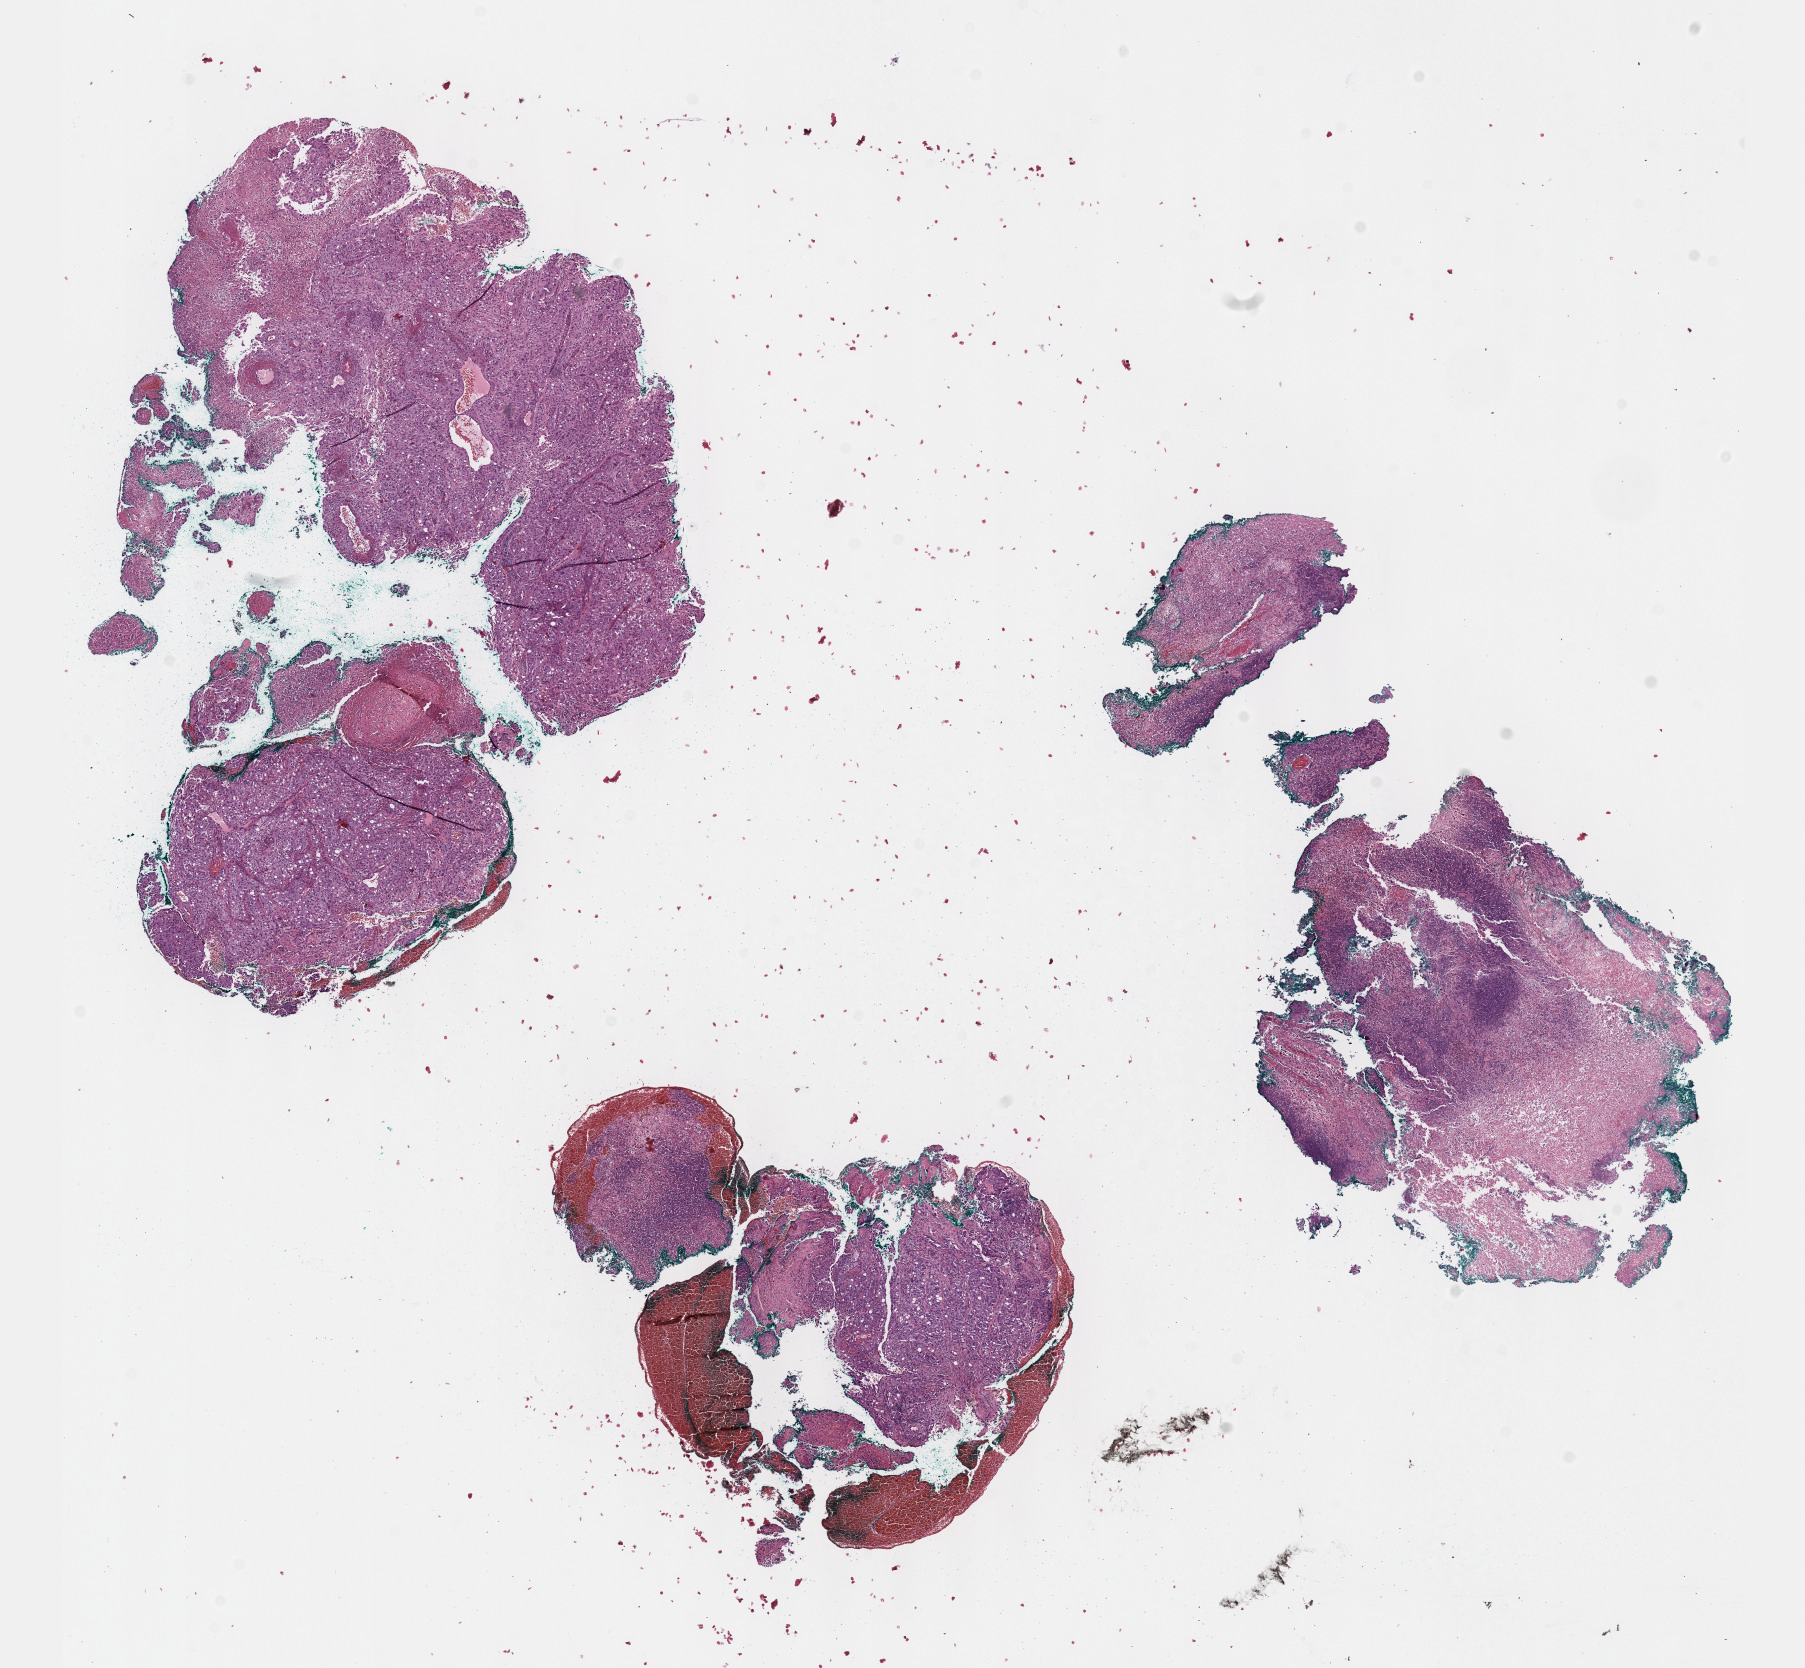
H&E whole-slide image — low-resolution overview of the scanned area, about 14.6 x 13.5 mm, formalin-fixed paraffin-embedded (FFPE) diagnostic section, cervix, primary tumour sample. Female patient; age at initial diagnosis 47 years. Histologic grade: GX (grade cannot be assessed).
- histologic diagnosis: Squamous cell carcinoma, NOS (cervix uteri)
- FIGO stage: IIB